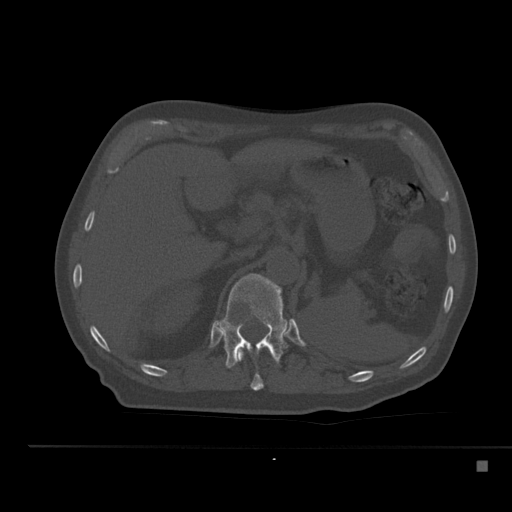
CT including the spine, one axial slice. Slice 232 of 517 in the series (ordered by position). 120 kVp. Bone window (W 1800 / L 400 HU). 512 × 512 image matrix, field of view 408 × 408 mm. Patient: male, 70 years. From the clinical record (not read from this slice): primary cancer: renal.
Structures marked on this image (semi-automatic segmentation, software-assisted and operator-edited):
- T11 vertebra: box from (x=237, y=348) to (x=273, y=391) px
- T12 vertebra: (x=214, y=274)–(x=290, y=368)